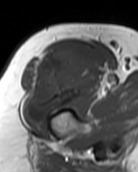
MRI of an extremity soft-tissue mass, one axial slice; slice 75 of 99 in the series (ordered by position); MR volume resampled by the dataset authors to the PET/CT grid (not the native acquisition matrix); 138 × 172 image matrix, field of view 135 × 168 mm. Female patient. From the clinical record (not read from this slice): histological type: pleiomorphic undifferentiated sarcoma; grade: high; site of the primary tumour: right quadricep.
Structures marked on this image (expert contour drawn on MRI and transferred to this co-registered scan by the dataset authors):
- gross tumour volume including surrounding oedema: bounding box (x1, y1, x2, y2) in pixels: (23, 45, 99, 122)
- gross tumour volume (mass): (23, 45, 99, 122)